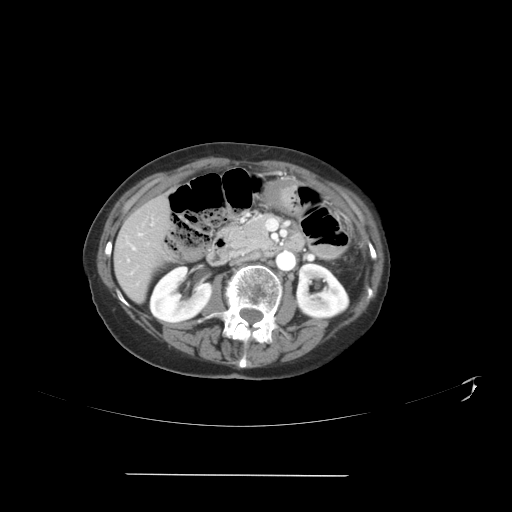
Contrast-enhanced abdominal CT, one axial slice. Slice 15 of 41 in the series (ordered by position). Reconstruction kernel STANDARD. 120 kVp. Soft-tissue window (W 400 / L 40 HU). 512 × 512 image matrix, field of view 431 × 431 mm. Female patient, age 74 years. Case-level facts recorded for this patient, not image findings: diagnosis: colorectal cancer liver metastases, imaged before liver resection; multiple liver metastases: yes; largest metastasis: 3.3 cm.
Outlined on this slice (expert manual segmentation):
- hepatic veins: box from (x=127, y=233) to (x=142, y=262) px
- liver: (x=116, y=198)–(x=166, y=299)
- planned liver remnant (the part of the liver to remain after resection): (x=120, y=198)–(x=166, y=245)
- portal vein (with intrahepatic branches): (x=130, y=244)–(x=135, y=250)